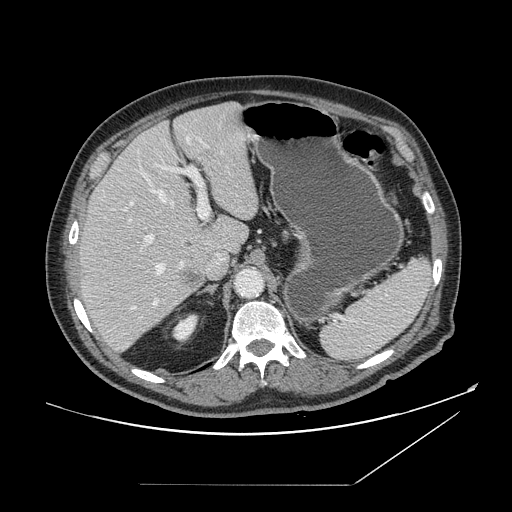
Contrast-enhanced abdominal CT, one axial slice; slice 105 of 166 in the series (ordered by position); 120 kVp; intravenous contrast given; soft-tissue window (W 400 / L 40 HU); 512 × 512 image matrix, field of view 416 × 416 mm. Male patient, age 80 years. Case-level facts recorded for this patient, not image findings: diagnosis: colorectal cancer liver metastases, imaged before liver resection; multiple liver metastases: no; largest metastasis: 2.2 cm; disease in both lobes: no.
Structures marked on this image (outlined manually by an expert reader):
- hepatic veins: bounding box [x1, y1, x2, y2] px = [130, 137, 190, 310]
- liver: [80, 103, 259, 353]
- planned liver remnant (the part of the liver to remain after resection): [88, 103, 258, 258]
- portal vein (with intrahepatic branches): [130, 165, 210, 305]
- liver metastasis: [185, 272, 204, 290]
- liver metastasis: [181, 269, 208, 287]